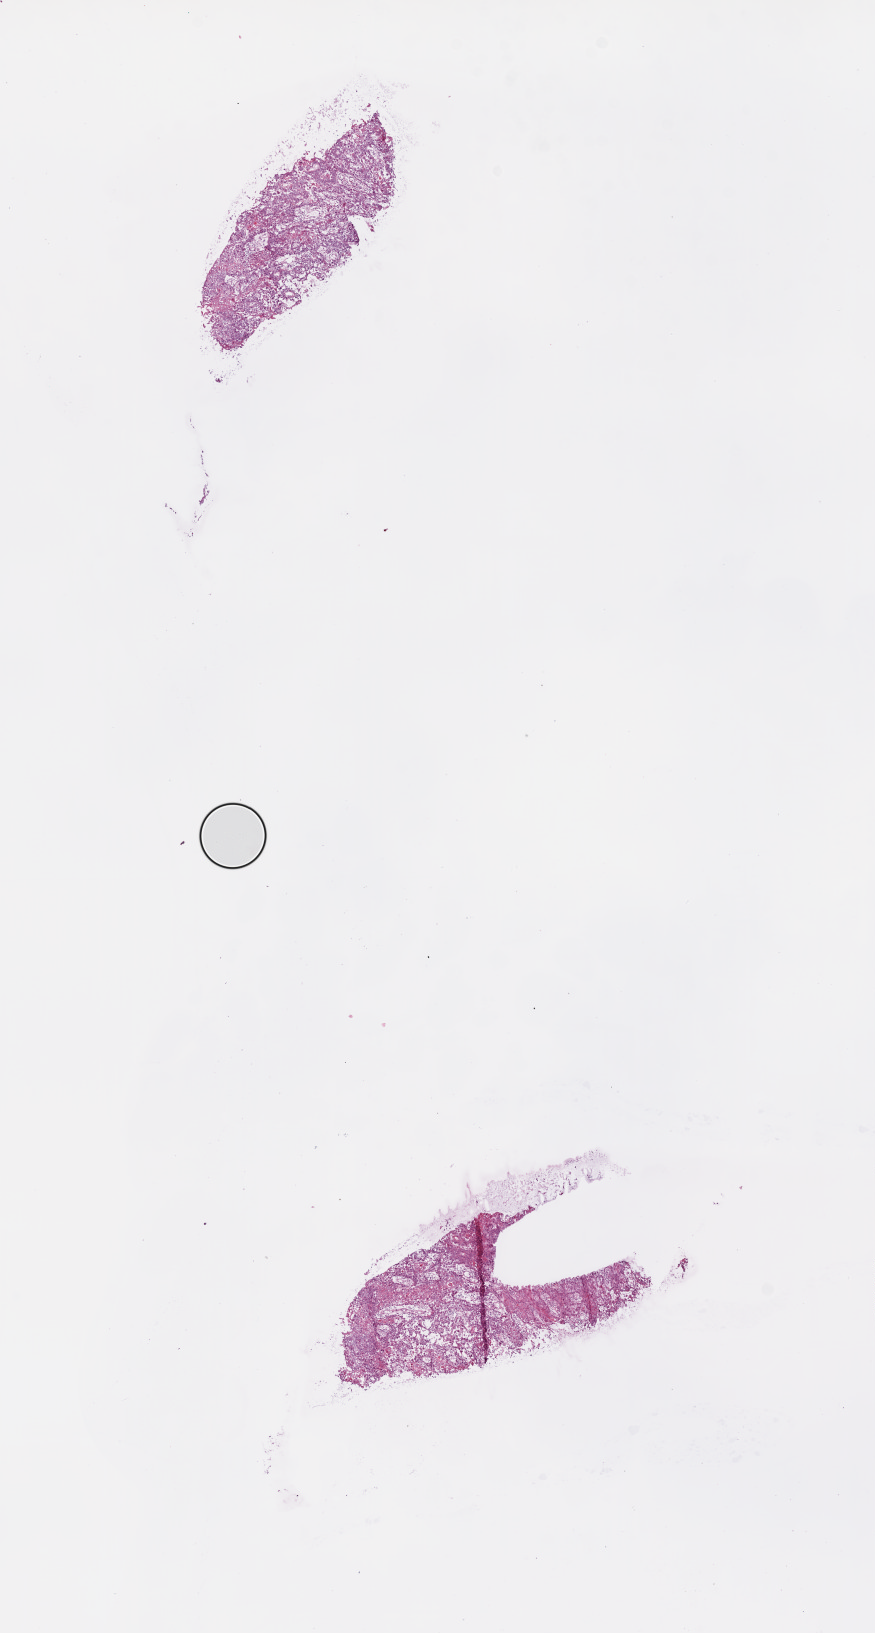
Digitized Hematoxylin and eosin (H&E) stained tissue section (whole slide), low-resolution overview of the scanned area, about 7.0 x 13.1 mm (acquisition: 20x scan); frozen section from the bottom of the tissue portion; head and neck, primary tumour sample. Male patient; age at initial diagnosis 56 years. Slide review estimates, as recorded: tumour cells 95%, tumour nuclei 80%.
Diagnosis: Squamous cell carcinoma, NOS.